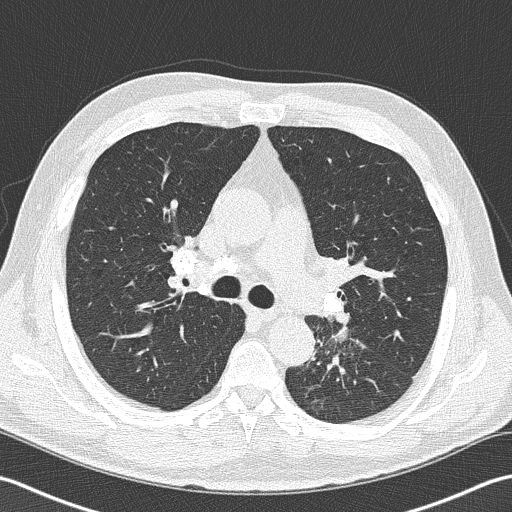
Low-dose screening chest CT, axial slice; second screening round (one year after baseline); lung window (W 1500 / L -600 HU); 512 × 512 image matrix, field of view 350 × 350 mm. Male, age 57 years at enrolment. Former smoker at enrolment.
Lesion marked by an expert reader, bounding box <294,313,375,387> (left, top, right, bottom; pixels). The exam's reader record, not a measurement of the box and not confirmed to be the same lesion: non-calcified nodule or mass ≥4 mm, left lower lobe, 40 × 30 mm, spiculated (stellate) margins, soft tissue attenuation, pre-existing on the prior screen: no. Official screen result: positive, other.